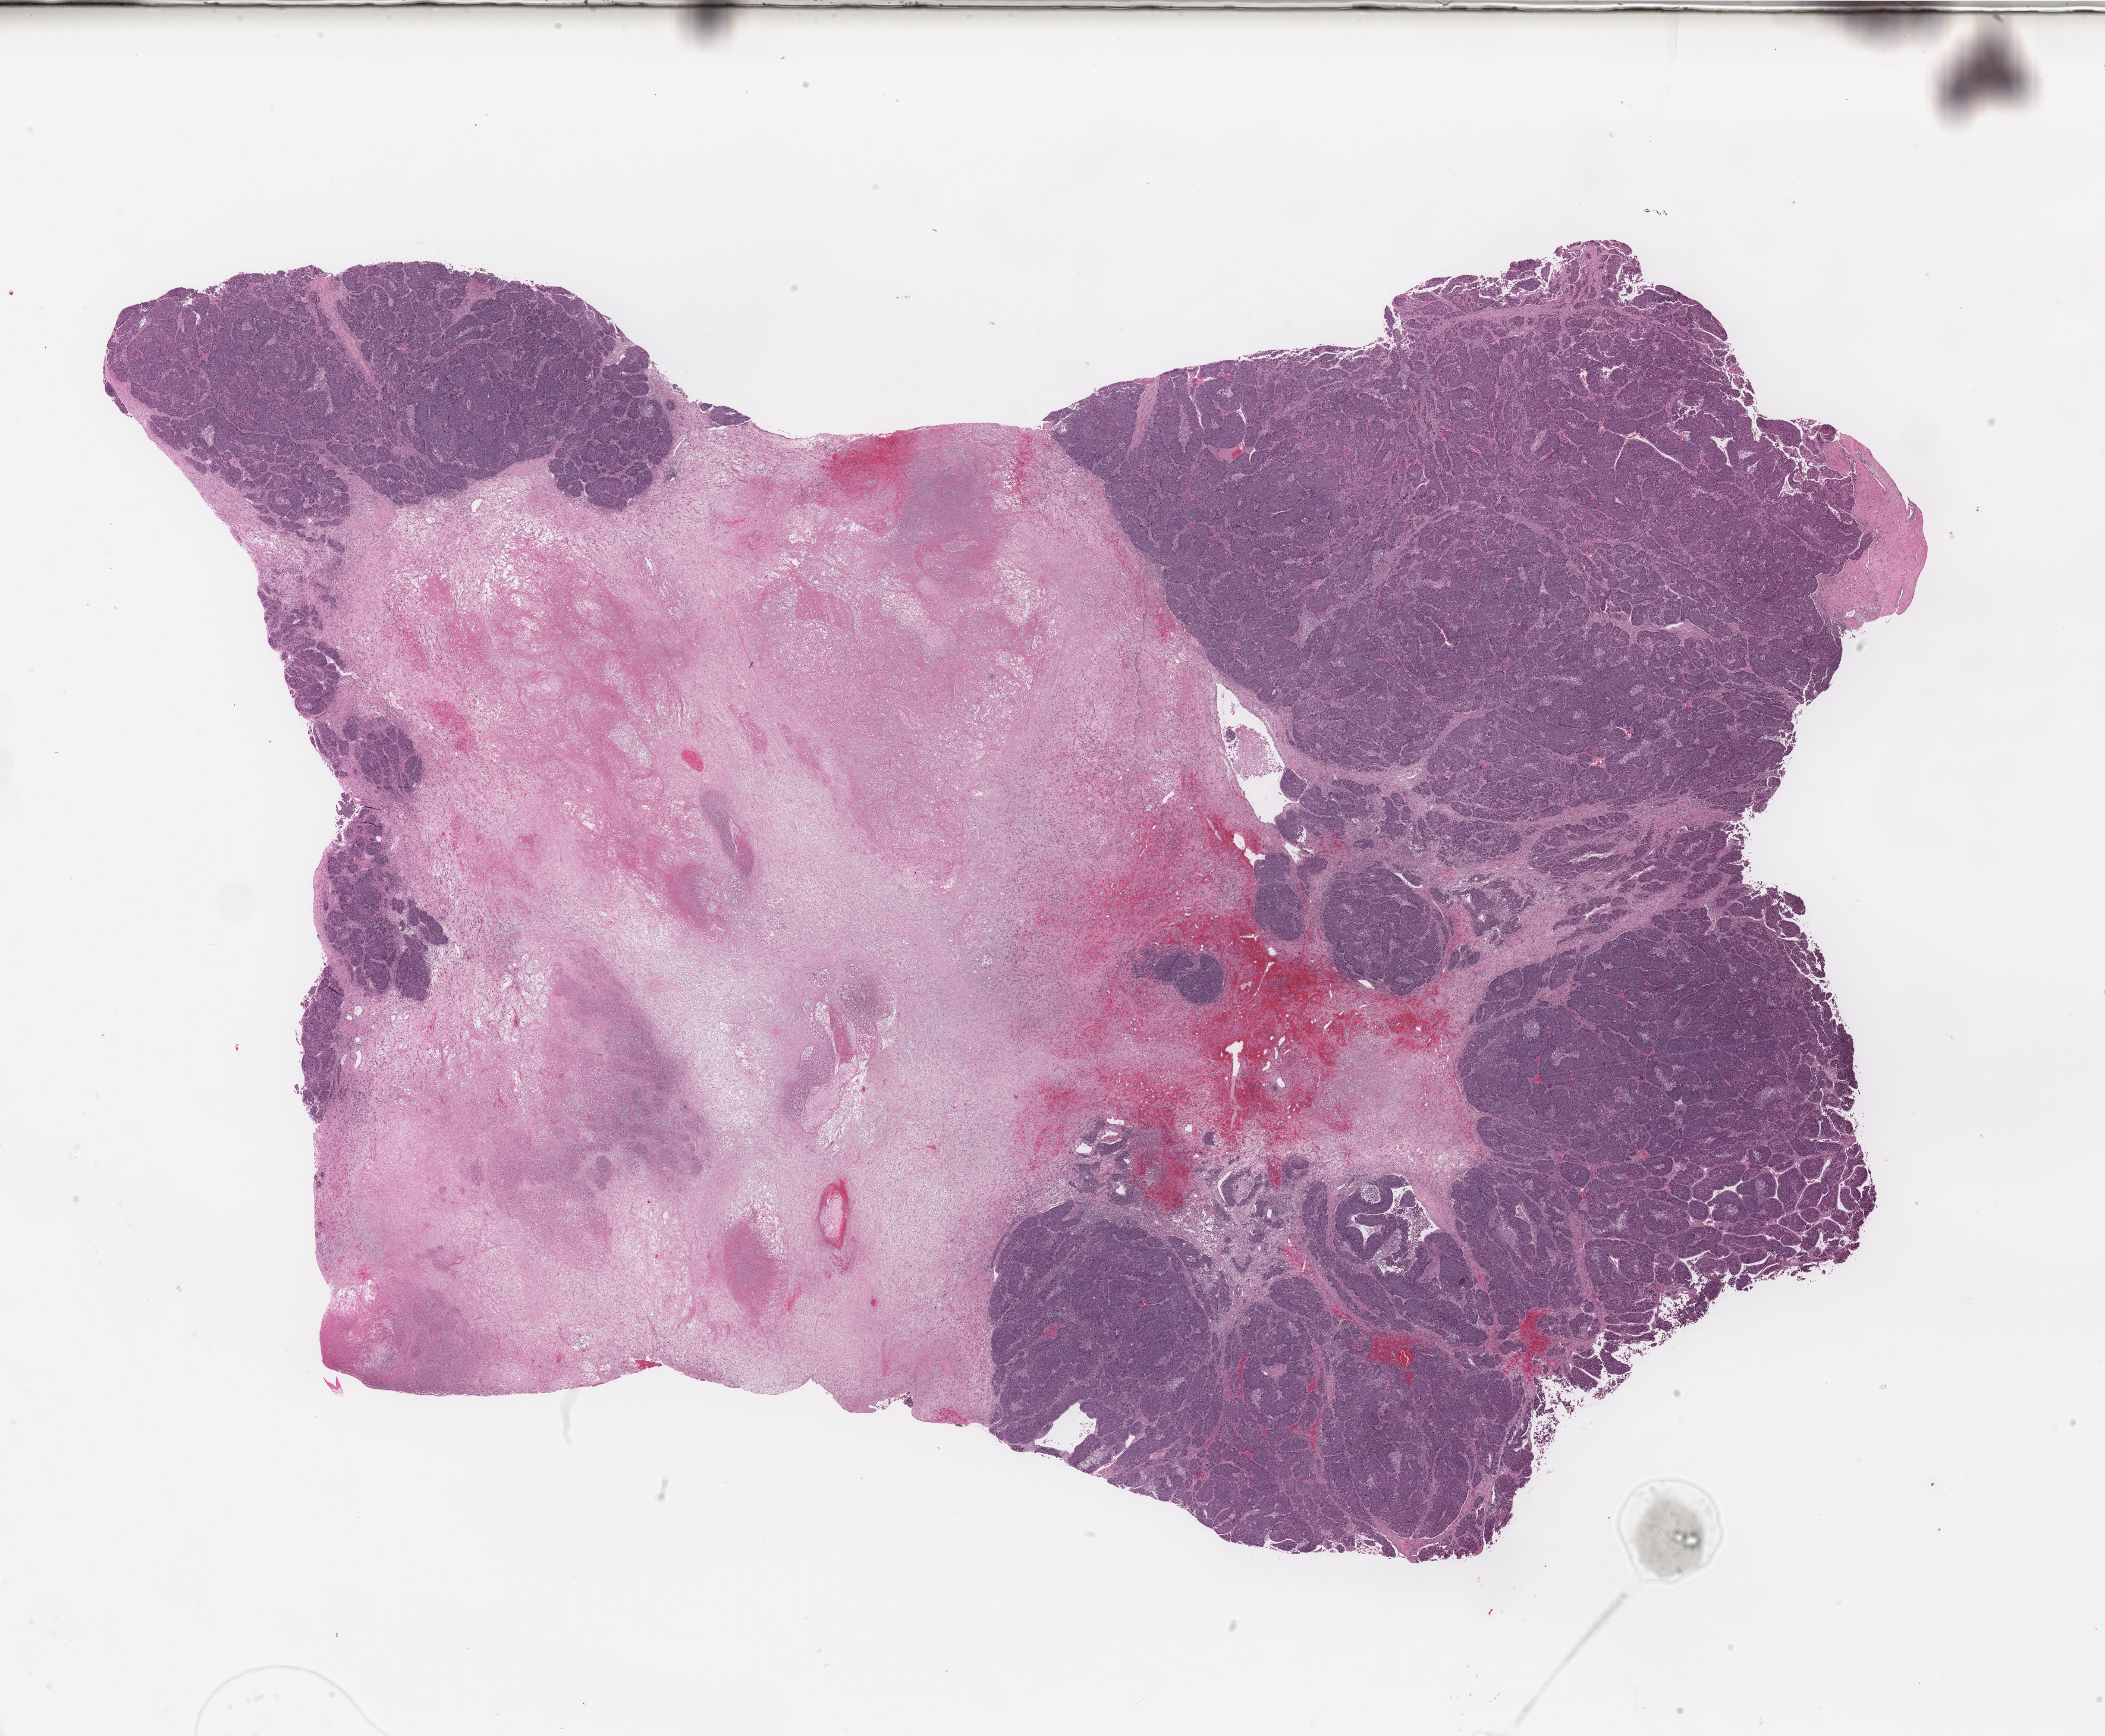
Digitized Hematoxylin and eosin (H&E) stained tissue section (whole slide) — a low-resolution overview of the entire scanned area, about 28.0 x 23.1 mm (slide scanned at 40x); FFPE section; sample: primary tumour, liver. Male, age 64 years at initial diagnosis. Histologic grade: G3 (poorly differentiated).
TNM: T2 NX M0. AJCC pathologic stage: II (7th edition). Histologic diagnosis: Hepatocellular carcinoma, NOS.